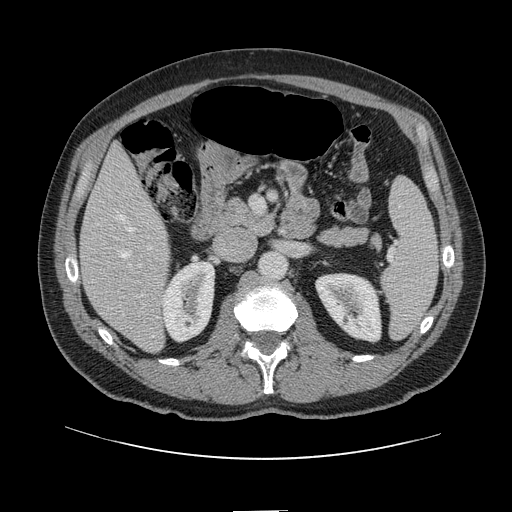
Contrast-enhanced abdominal CT, one axial slice; slice 51 of 161 in the series (ordered by position); 120 kVp; intravenous contrast given; soft-tissue window (W 400 / L 40 HU); 2.5 mm slice thickness; 512 × 512 image matrix, field of view 412 × 412 mm. Male patient, age 66 years. Case-level facts recorded for this patient, not image findings: diagnosis: colorectal cancer liver metastases, imaged before liver resection; multiple liver metastases: no; largest metastasis: 3.5 cm; disease in both lobes: no.
Outlined on this slice (outlined manually by an expert reader):
- hepatic veins: bounding box <116,214,134,258> (left, top, right, bottom; pixels)
- liver: <81,147,169,351>
- planned liver remnant (the part of the liver to remain after resection): <81,148,162,276>
- portal vein (with intrahepatic branches): <128,245,154,298>